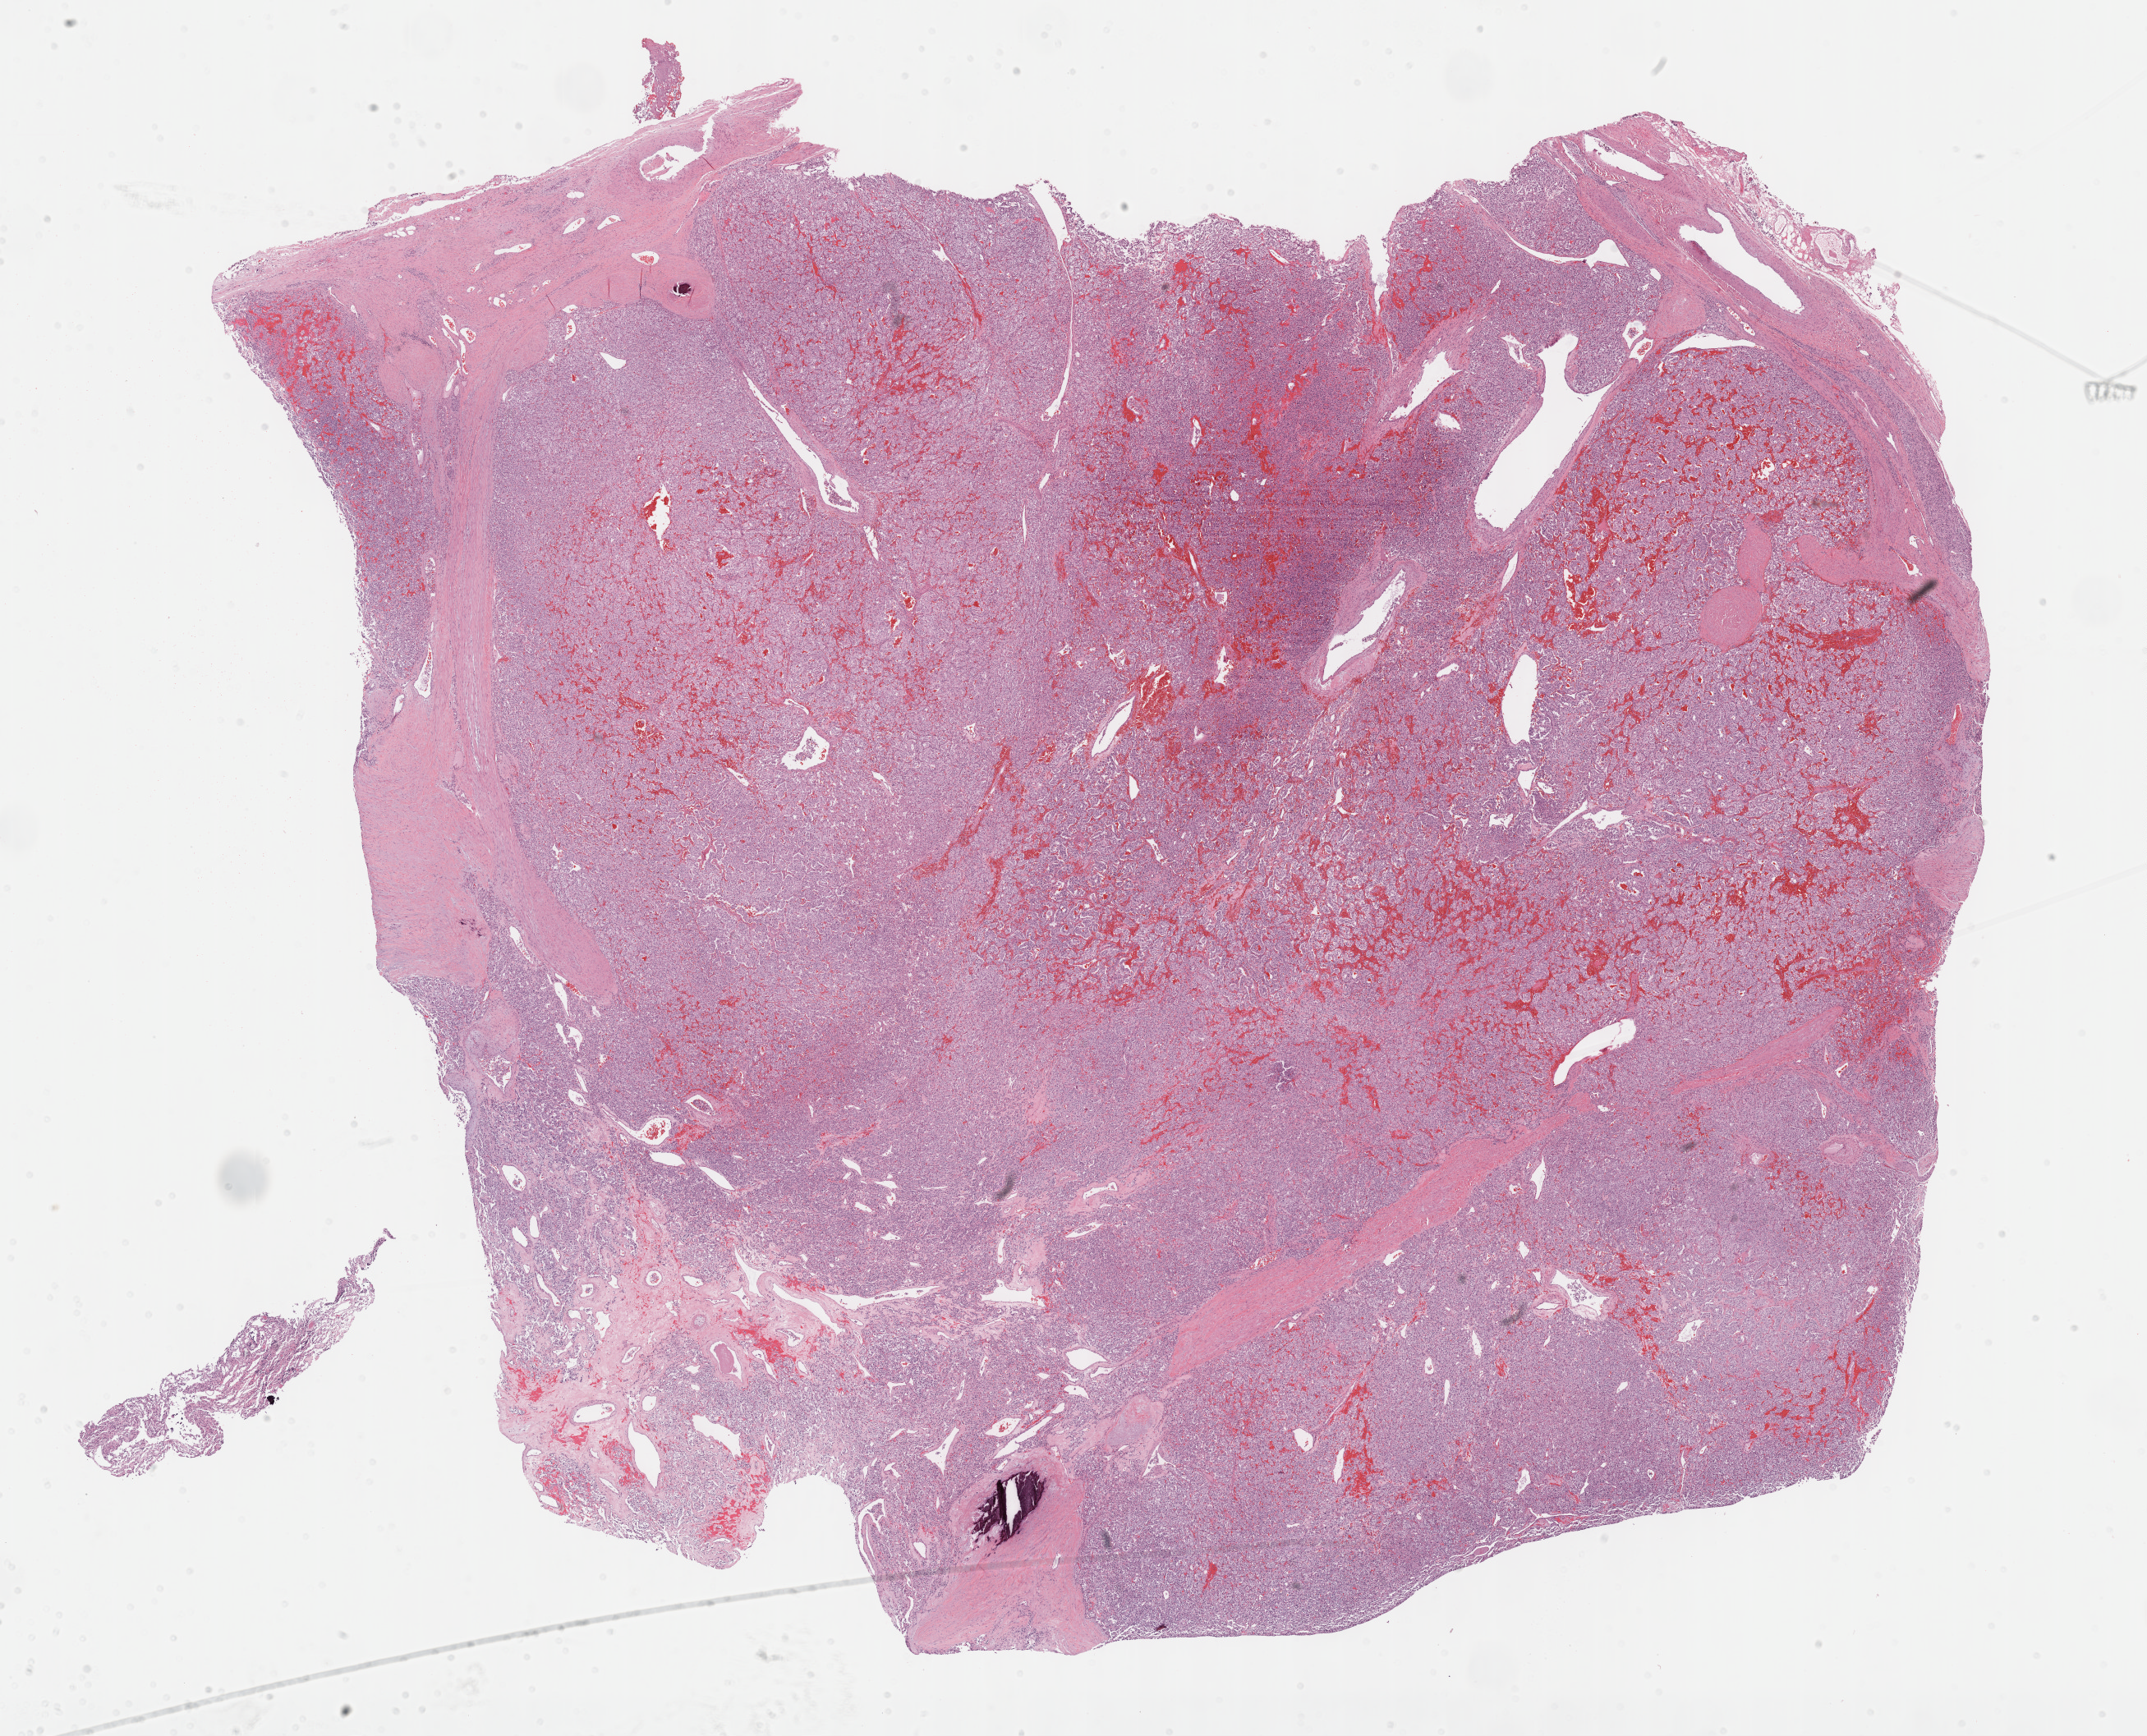
Whole-slide histology image, H&E-stained, low-resolution overview of the scanned area, about 21.1 x 17.1 mm (from a 40x scan); formalin-fixed paraffin-embedded (FFPE) diagnostic section; primary tumour sample from the connective, subcutaneous and other soft tissues. Female patient; age at initial diagnosis 57 years.
Histologic diagnosis: Paraganglioma, NOS (connective, subcutaneous and other soft tissues of abdomen).